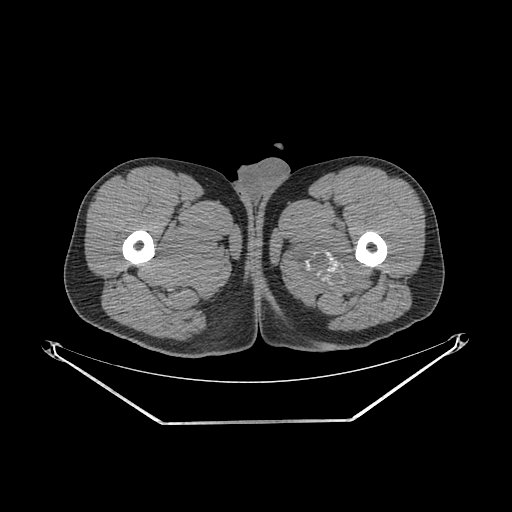
CT of an extremity soft-tissue mass (from a PET/CT study), one axial slice; position 258 of 267 along the scan axis; soft-tissue window (W 400 / L 40 HU); 3.75 mm slice thickness; 512 × 512 image matrix. Male patient. From the clinical record (not read from this slice): histological type: extraskeletal osteosarcoma; grade: high; site of the primary tumour: left adductur.
Outlined on this slice (expert contour drawn on MRI and transferred to this co-registered scan by the dataset authors):
- gross tumour volume (mass): bounding box <290,210,378,302> (left, top, right, bottom; pixels)